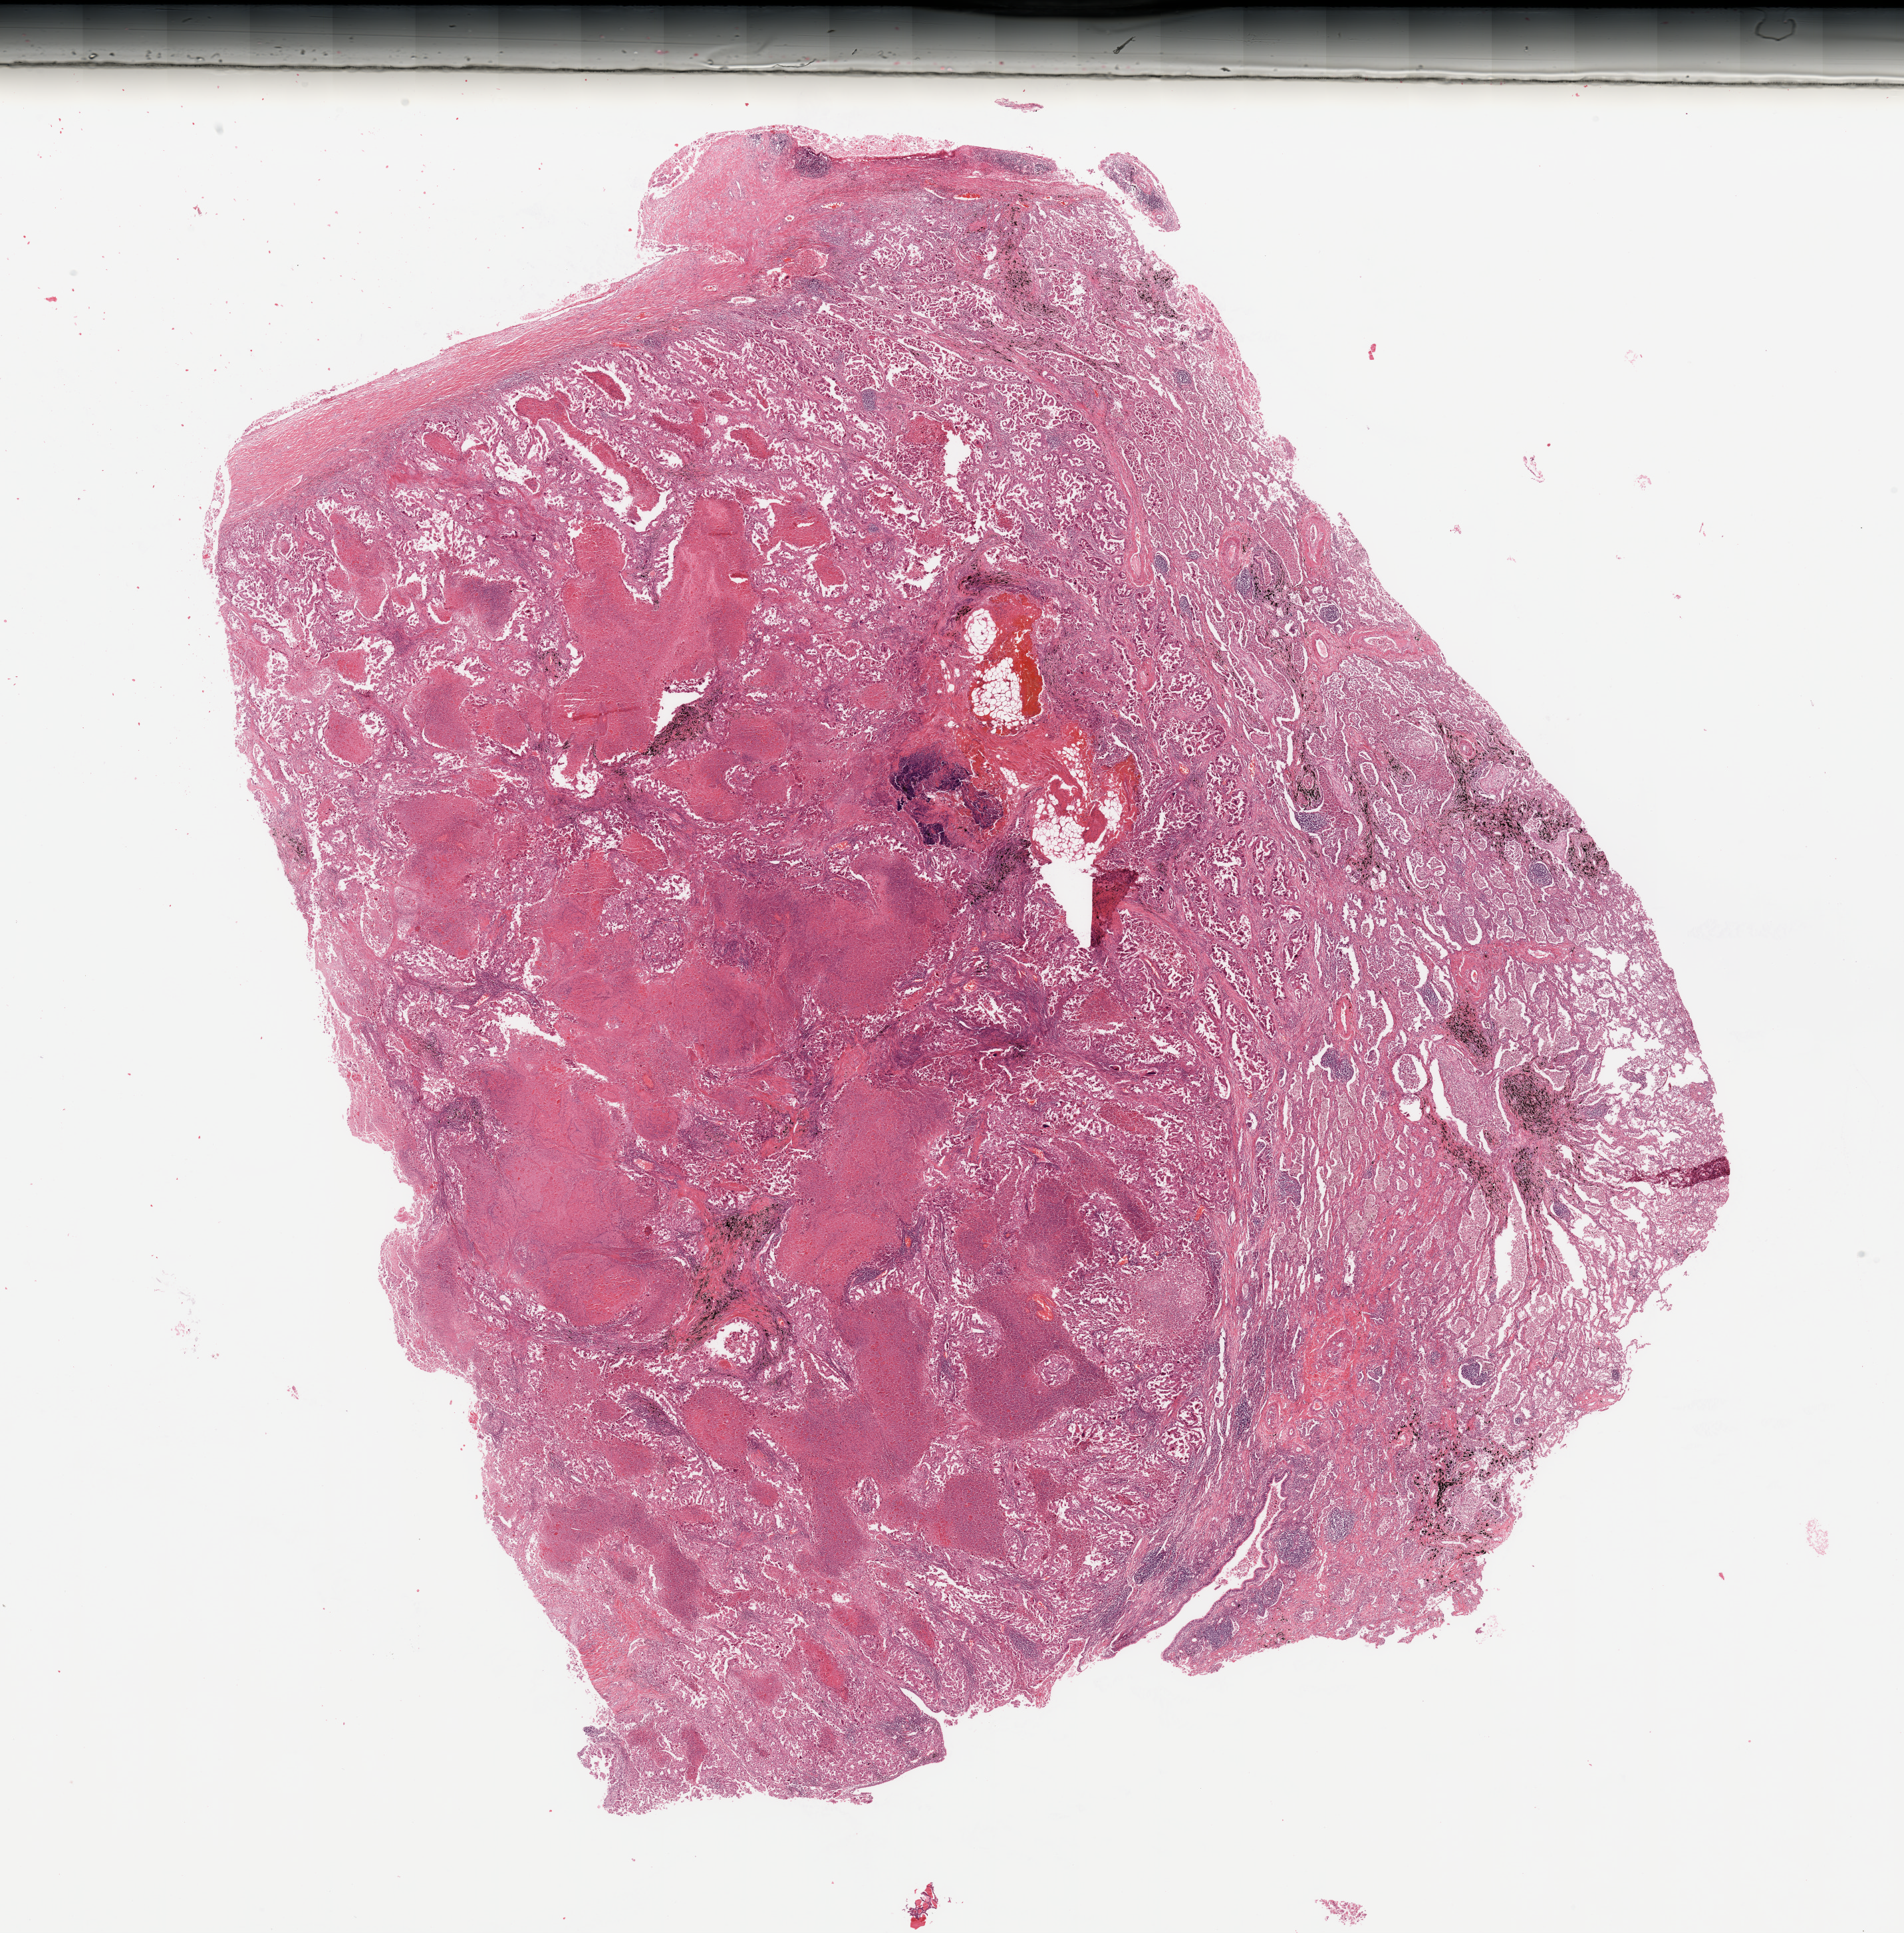
Whole-slide histology image, H&E-stained — low-resolution overview of the scanned area, about 22.6 x 23.0 mm (acquisition: 20x scan). Tumour tissue sample, lung. 54-year-old male patient. Histologic grade: G2 (moderately differentiated).
Diagnosis: Adenocarcinoma, NOS. AJCC pathologic stage: IB.